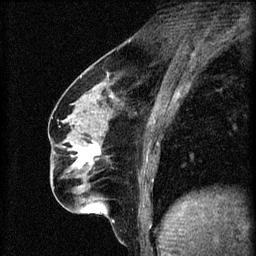
Breast MRI (dynamic contrast-enhanced), one sagittal slice. Slice 26 of 60 in the series (ordered by position). 3 images stored at this slice position (order not interpretable as contrast timing). 1.5 T. TE 4.2 ms, TR 8.2 ms. 2 mm slice thickness. 256 × 256 image matrix, field of view 180 × 180 mm. Patient: female, 56 years.
Annotated regions visible in this slice (semi-automatic segmentation, software-assisted and operator-edited):
- analysis volume of interest (the breast-tissue region the enhancement analysis was run in; not a lesion): bounding box [x1, y1, x2, y2] px = [62, 136, 111, 179]
- tumour enhancement mask (voxels above the 70 % enhancement threshold inside the analysis volume of interest): [76, 142, 100, 169]